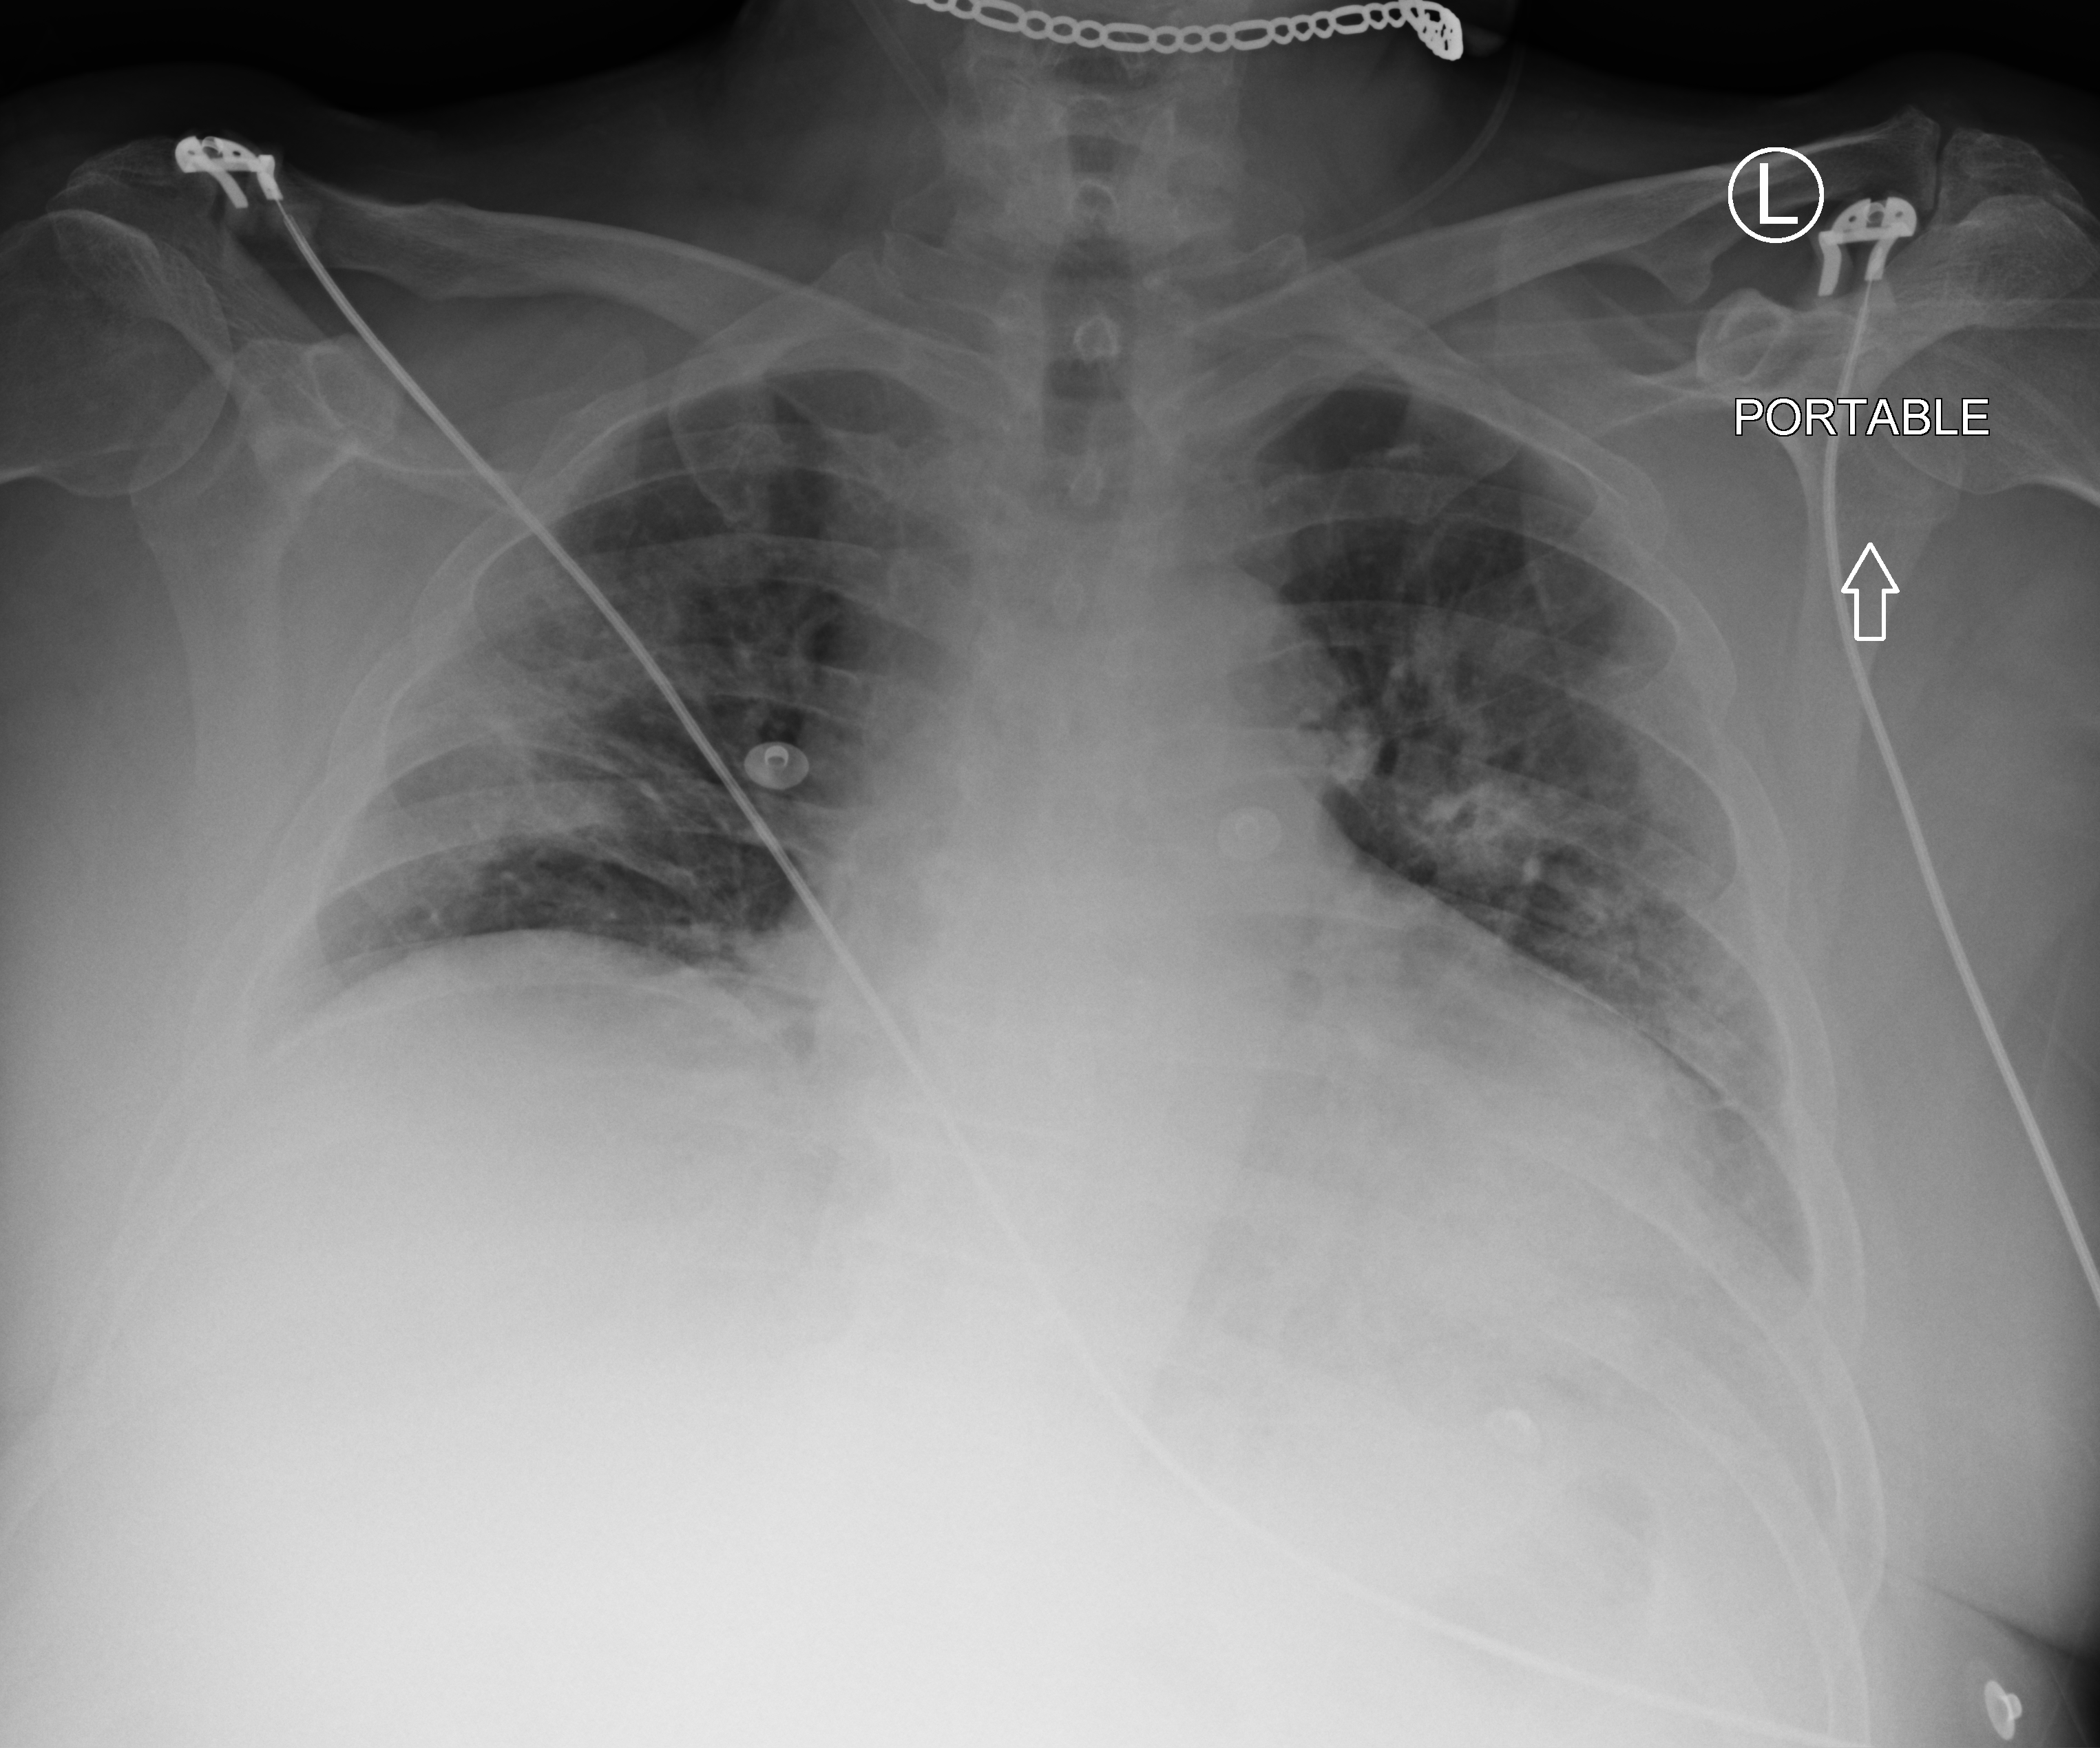
Chest X-ray (portable); anteroposterior (AP) projection. Patient hospitalised with COVID-19; male, aged 60–74 years.
From the hospital-stay record, not from the radiograph (when in the stay this image was taken is not recorded): admitted to intensive care during this hospital stay: no; length of hospital stay: 5 days.